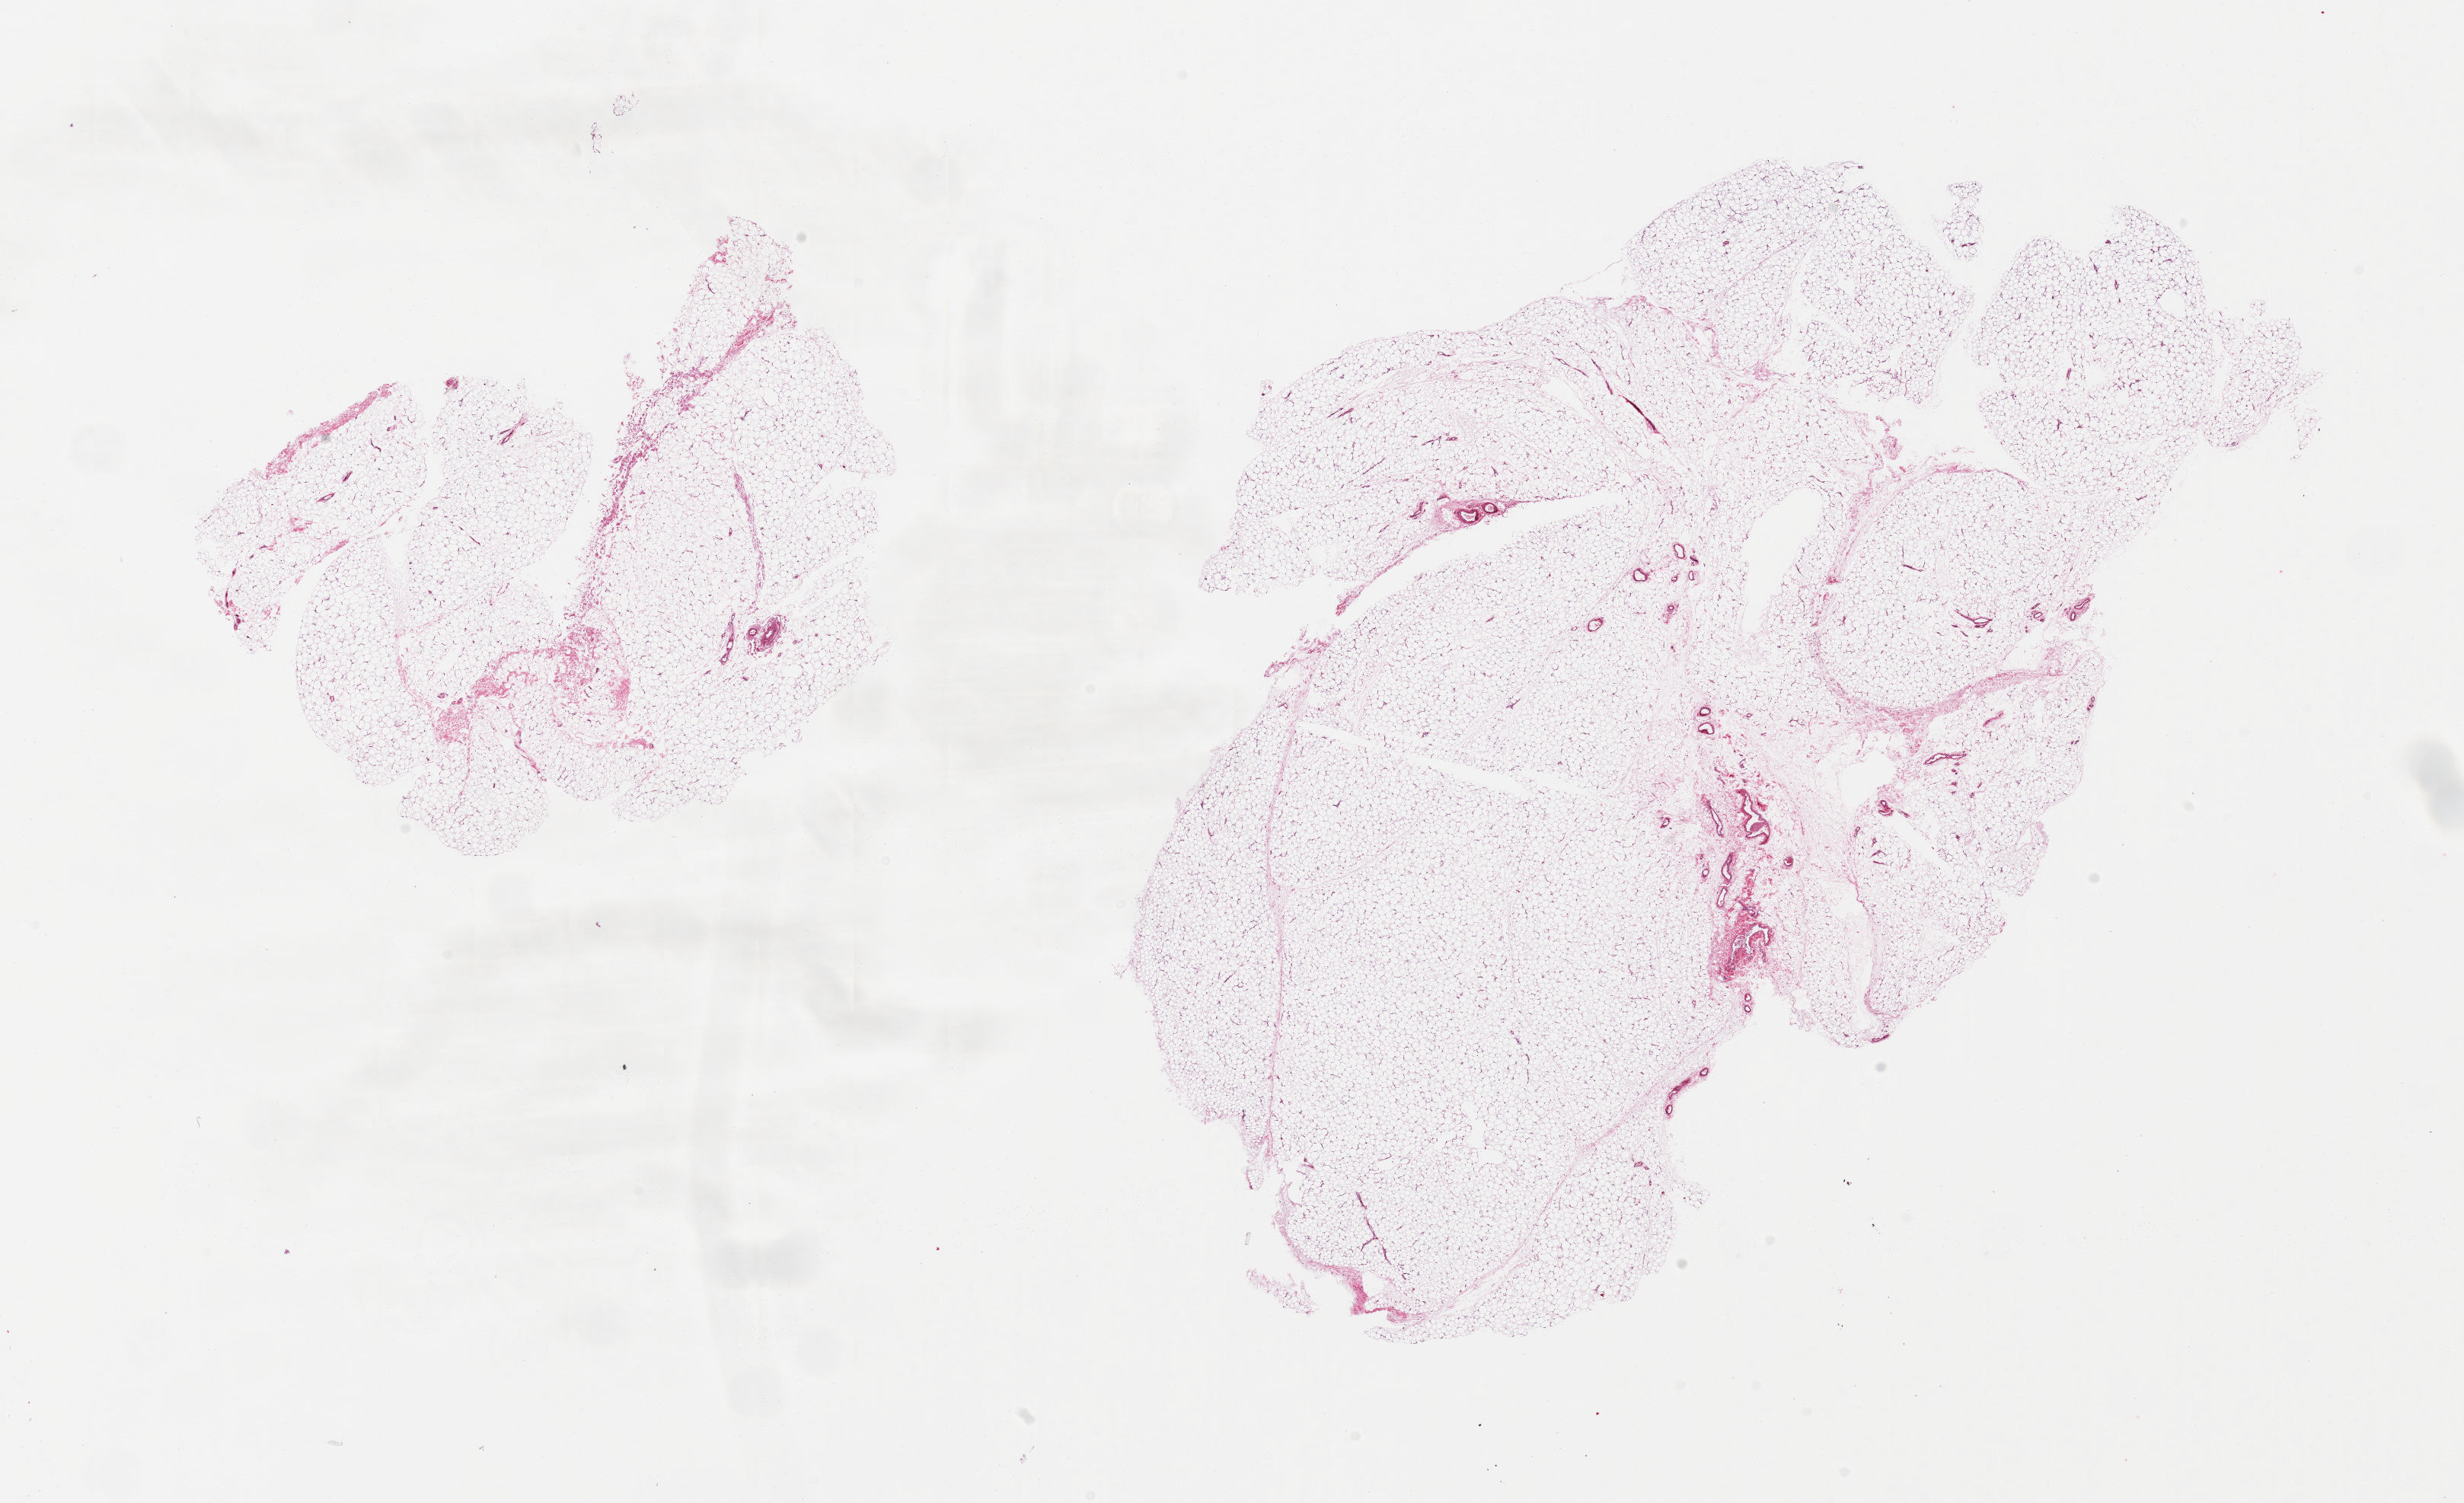
Hematoxylin and eosin (H&E) whole-slide image — shown as a low-resolution overview of the whole scanned area (about 25.6 x 15.6 mm); PAXgene-fixed paraffin-embedded (PFPE) section; sampled site (target tissue): adipose tissue; tissue donor sample. Donor: female.
• review note (as recorded): 2 pieces, trace fascia/vascular elements